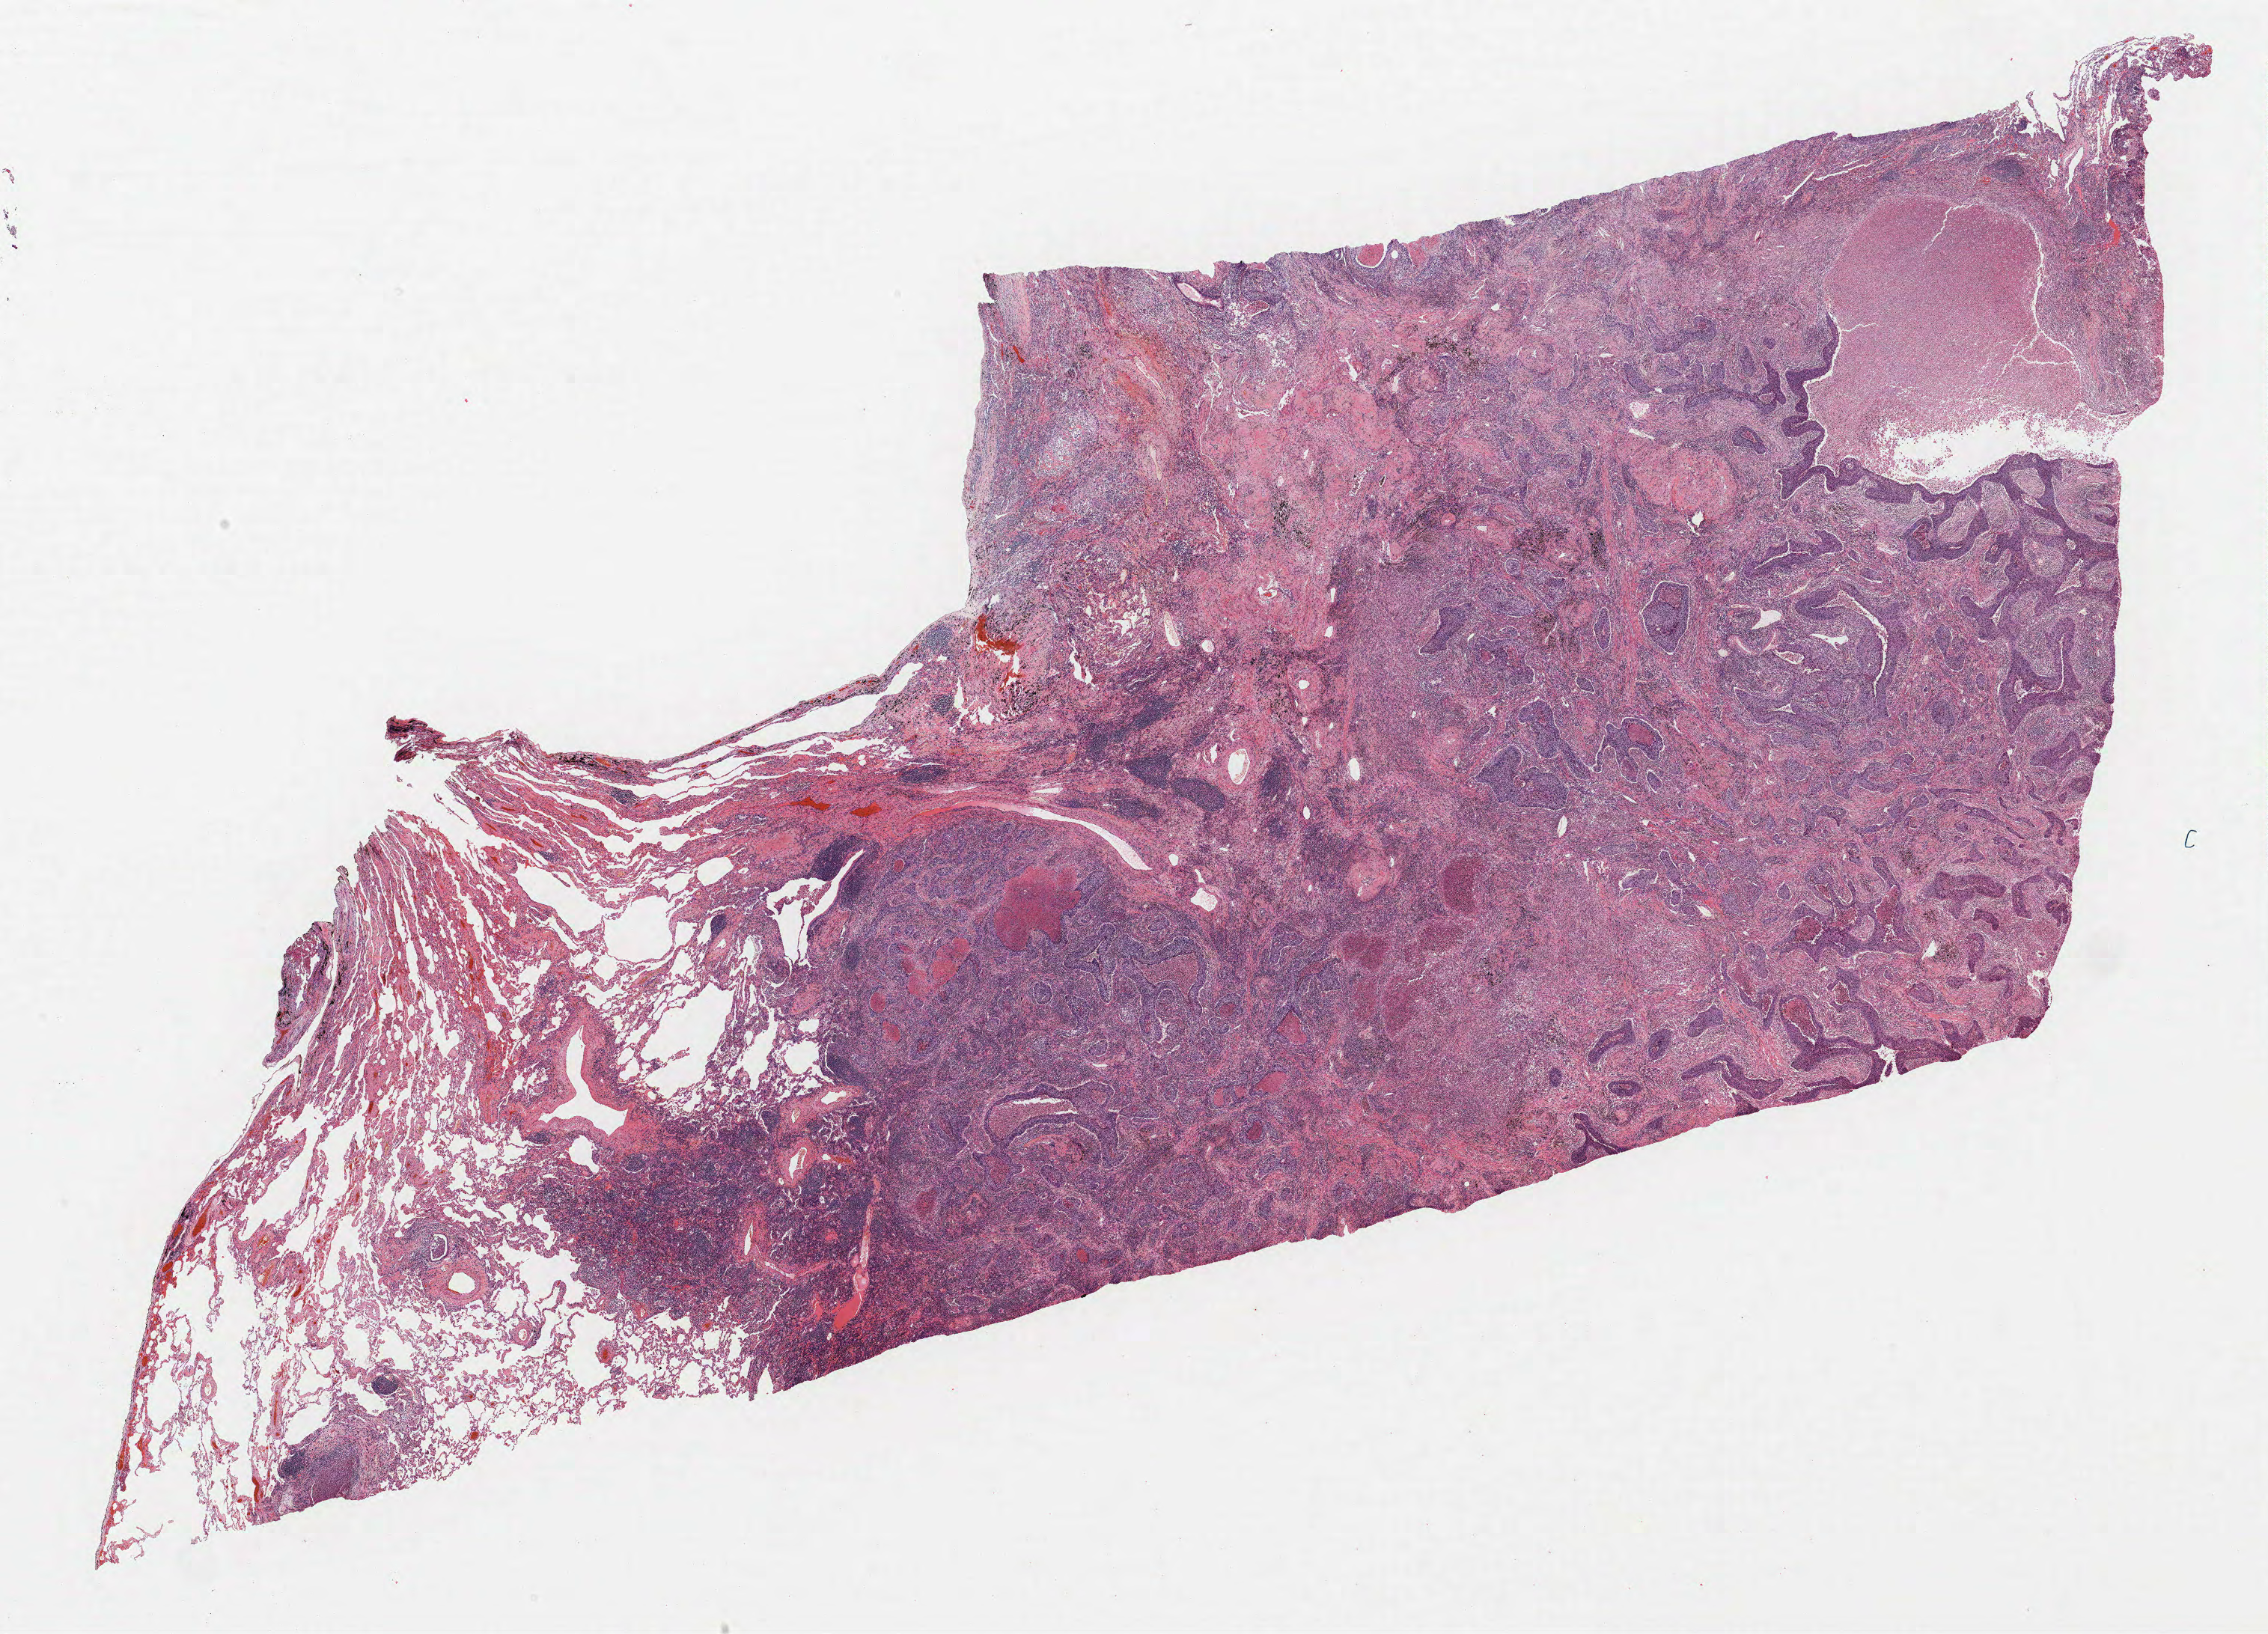
Whole-slide histology image, H&E-stained — whole scanned area (about 24.2 x 17.5 mm) shown as a low-resolution overview; formalin-fixed paraffin-embedded (FFPE) section; lung tissue. Female patient, aged 67 at enrolment. Grade: poorly differentiated (G3).
Participant's lung-cancer diagnosis: Squamous cell carcinoma, NOS. Tumour size (pathology): 50 mm. Primary tumour location (clinical record): left lower lobe. Stage (AJCC 6th edition): IB.